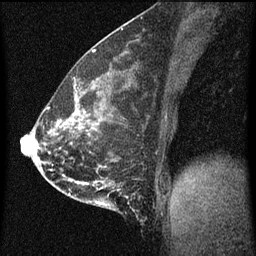
Breast MRI (dynamic contrast-enhanced), one sagittal slice; position 24 of 60 along the scan axis; dynamic contrast-enhanced series, image 2 of 3 at this slice position (ordered by acquisition); 1.5 T; TE 4.2 ms, TR 8 ms; 256 × 256 image matrix, field of view 180 × 180 mm. Female patient, age 35 years.
Annotated regions visible in this slice (semi-automatically segmented with operator editing):
- analysis volume of interest (the breast-tissue region the enhancement analysis was run in; not a lesion): bounding box [x1, y1, x2, y2] px = [110, 180, 144, 219]
- tumour enhancement mask (voxels above the 70 % enhancement threshold inside the analysis volume of interest): [110, 184, 121, 191]